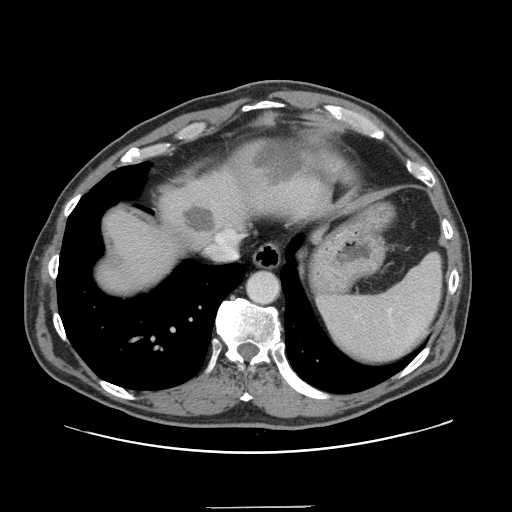
Contrast-enhanced abdominal CT, one axial slice; position 126 of 139 along the scan axis; soft-tissue window (W 400 / L 40 HU); 2.5 mm slice thickness; 512 × 512 image matrix. Male patient, age 64 years. From the clinical record (not read from this slice): diagnosis: colorectal cancer liver metastases, imaged before liver resection; multiple liver metastases: yes; largest metastasis: 3.5 cm; disease in both lobes: yes.
Annotated regions visible in this slice (manually delineated by an expert):
- liver: box from (x=96, y=139) to (x=324, y=293) px
- planned liver remnant (the part of the liver to remain after resection): (x=96, y=148)–(x=251, y=293)
- liver metastasis: (x=184, y=209)–(x=215, y=235)
- liver metastasis: (x=254, y=143)–(x=304, y=187)